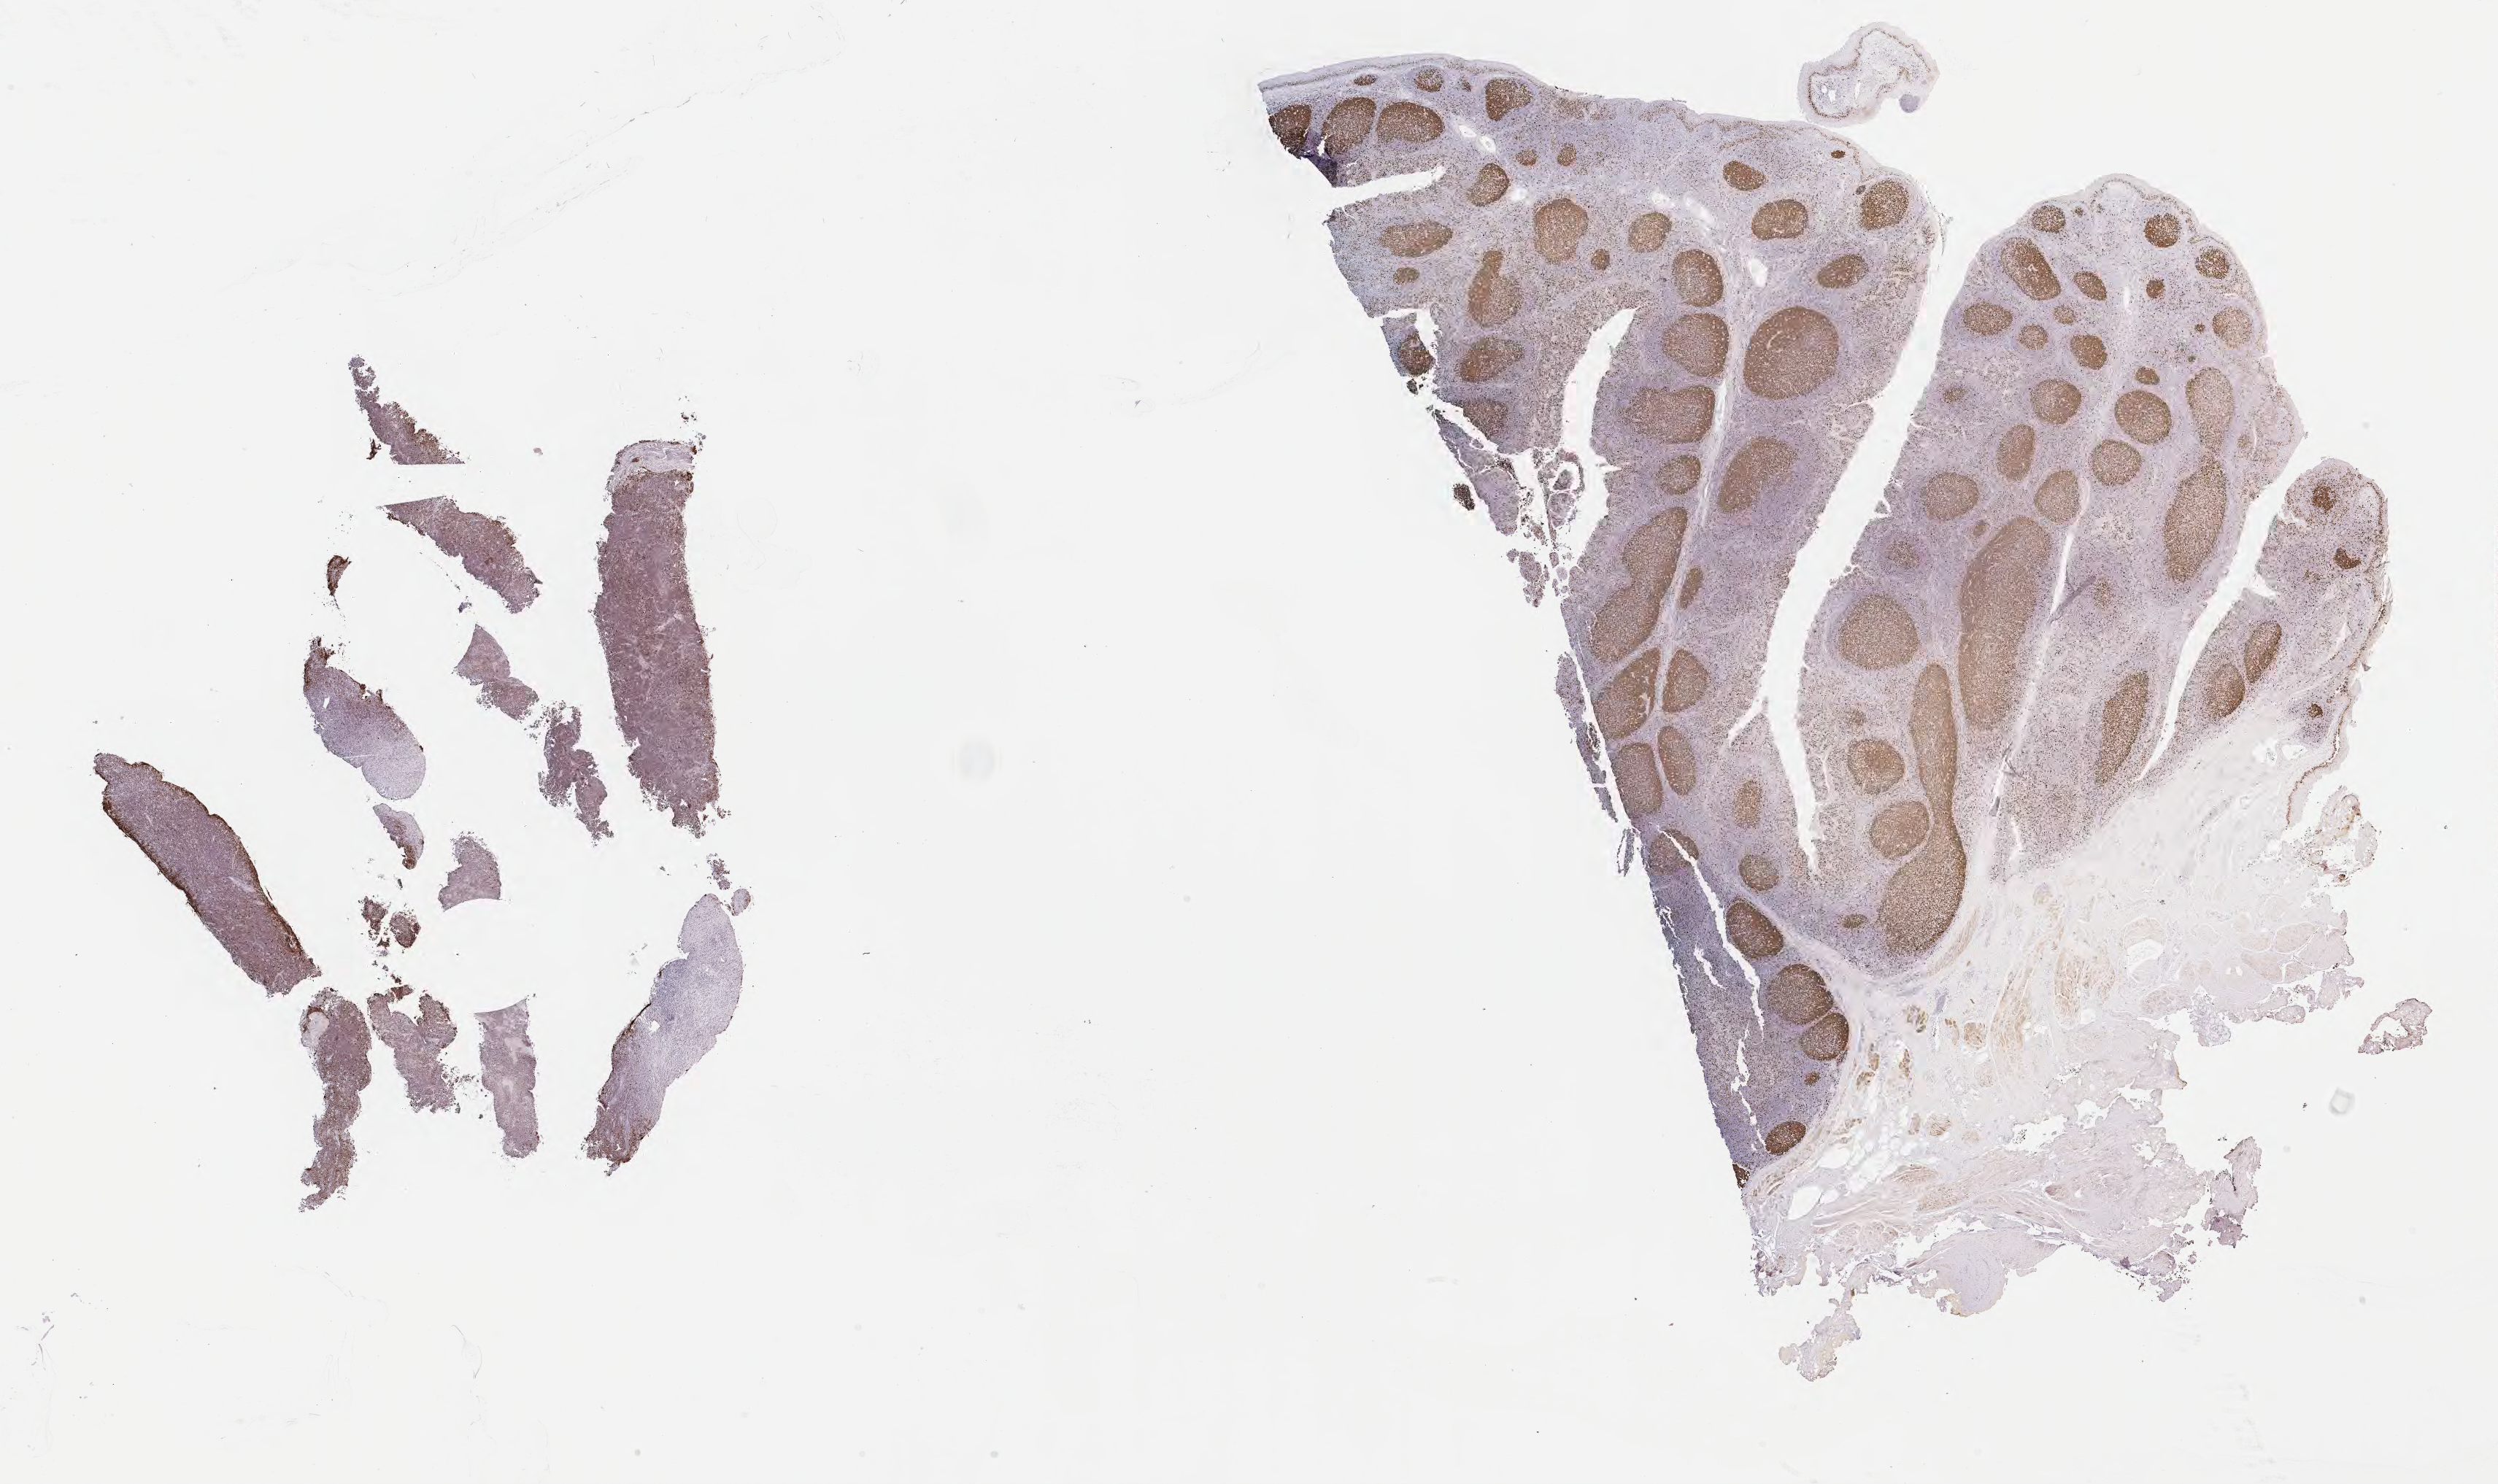
Whole-slide image, immunohistochemical stain for Ki-67, whole scanned area (about 27.7 x 16.5 mm) shown as a low-resolution overview; specimen: tumor tissue; anatomic site: abdomen proper. Male patient; age at initial diagnosis 7 years.
- histologic diagnosis: Burkitt lymphoma, NOS